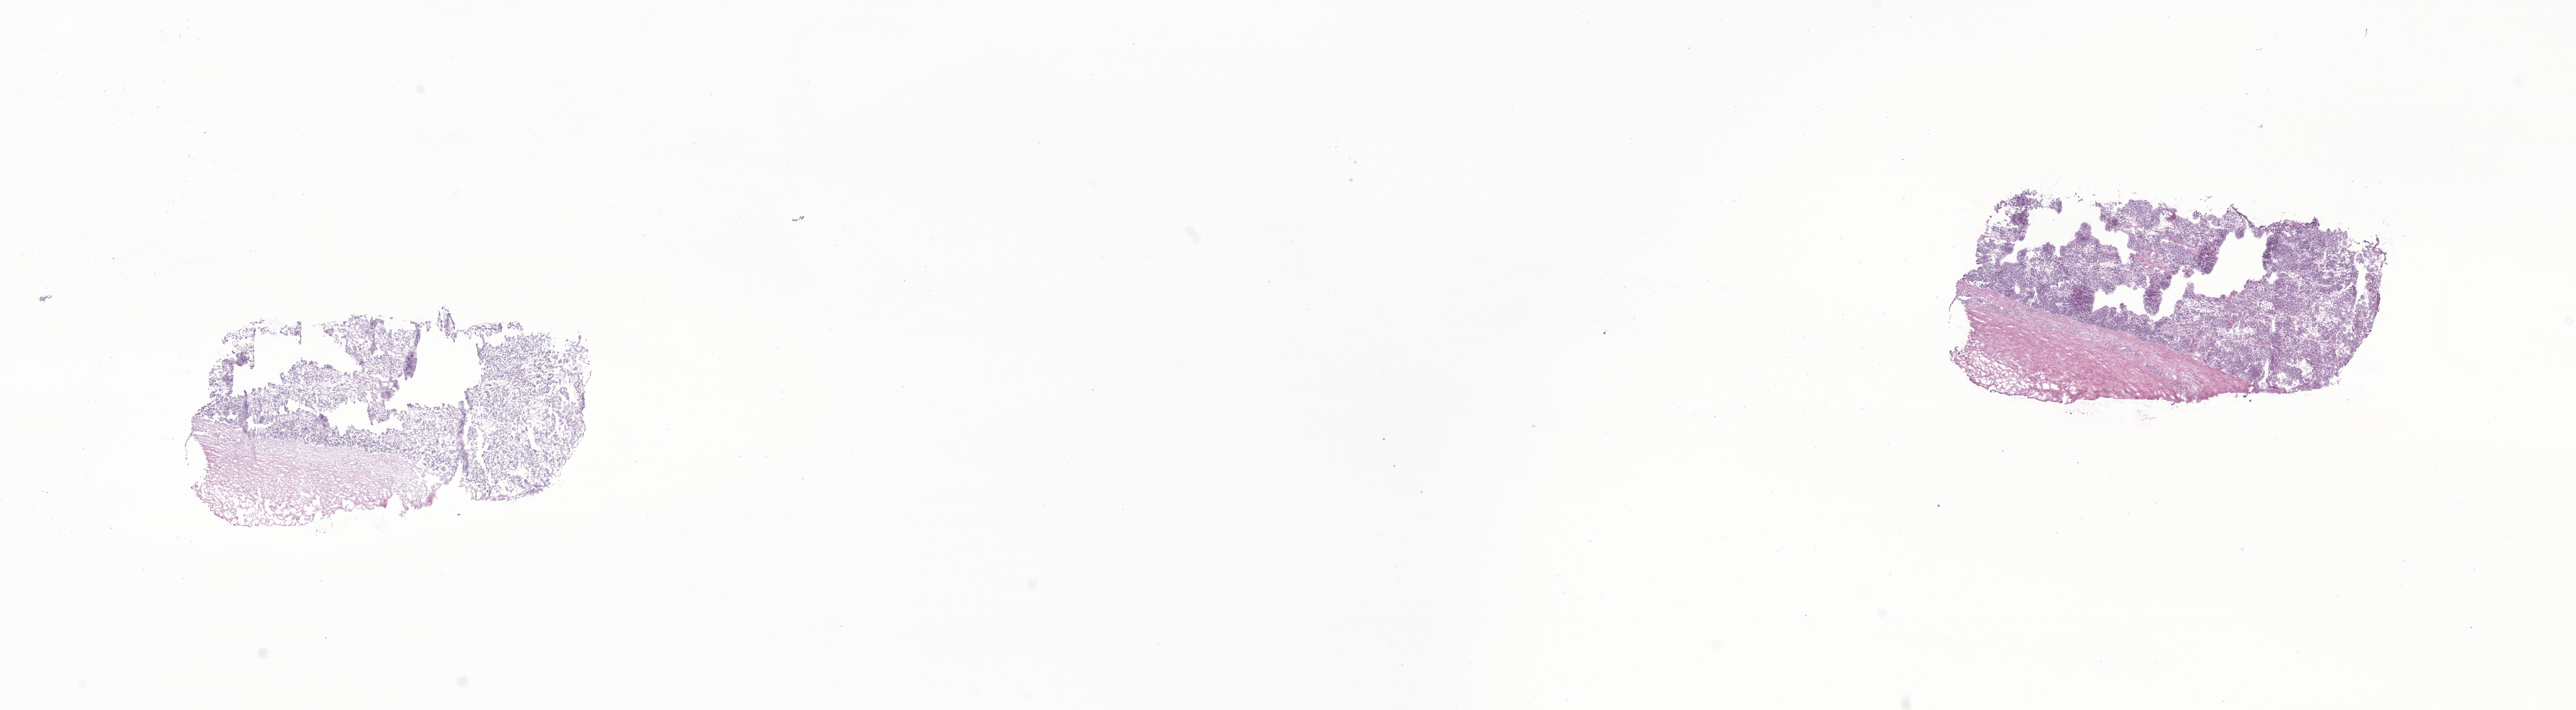
Digitized haematoxylin and eosin-stained section of tumor tissue from the abdomen — low-resolution overview of the scanned area, about 26.9 x 7.4 mm; cryosection (OCT / tissue freezing medium). Patient male; age 317 days.
Recorded diagnosis: Neuroblastoma, NOS.